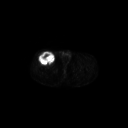
FDG PET of an extremity soft-tissue mass (from a PET/CT study), one axial slice. Position 284 of 311 along the scan axis. 3.27 mm slice thickness. 128 × 128 image matrix, field of view 700 × 700 mm. Patient: male, 56 years. Case-level facts recorded for this patient, not image findings: histological type: pleiomorphic leiomyosarcoma; grade: intermediate; site of the primary tumour: right thigh.
Annotated regions visible in this slice (expert contour drawn on MRI and transferred to this co-registered scan by the dataset authors):
- gross tumour volume including surrounding oedema: bounding box <38,52,55,65> (left, top, right, bottom; pixels)
- gross tumour volume (mass): <38,52,55,65>